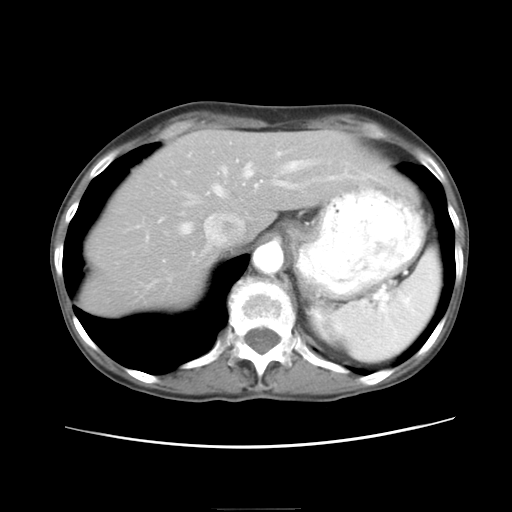
Contrast-enhanced abdominal CT, one axial slice. Slice 18 of 26 in the series (ordered by position). Reconstruction kernel STANDARD. Intravenous contrast given. Soft-tissue window (W 400 / L 40 HU). 512 × 512 image matrix, field of view 340 × 340 mm. Female patient, age 65 years. Case-level facts recorded for this patient, not image findings: diagnosis: colorectal cancer liver metastases, imaged before liver resection.
Outlined on this slice (outlined manually by an expert reader):
- hepatic veins: bounding box <181,160,310,233> (left, top, right, bottom; pixels)
- liver: <86,132,402,310>
- planned liver remnant (the part of the liver to remain after resection): <87,132,402,309>
- portal vein (with intrahepatic branches): <255,153,289,187>